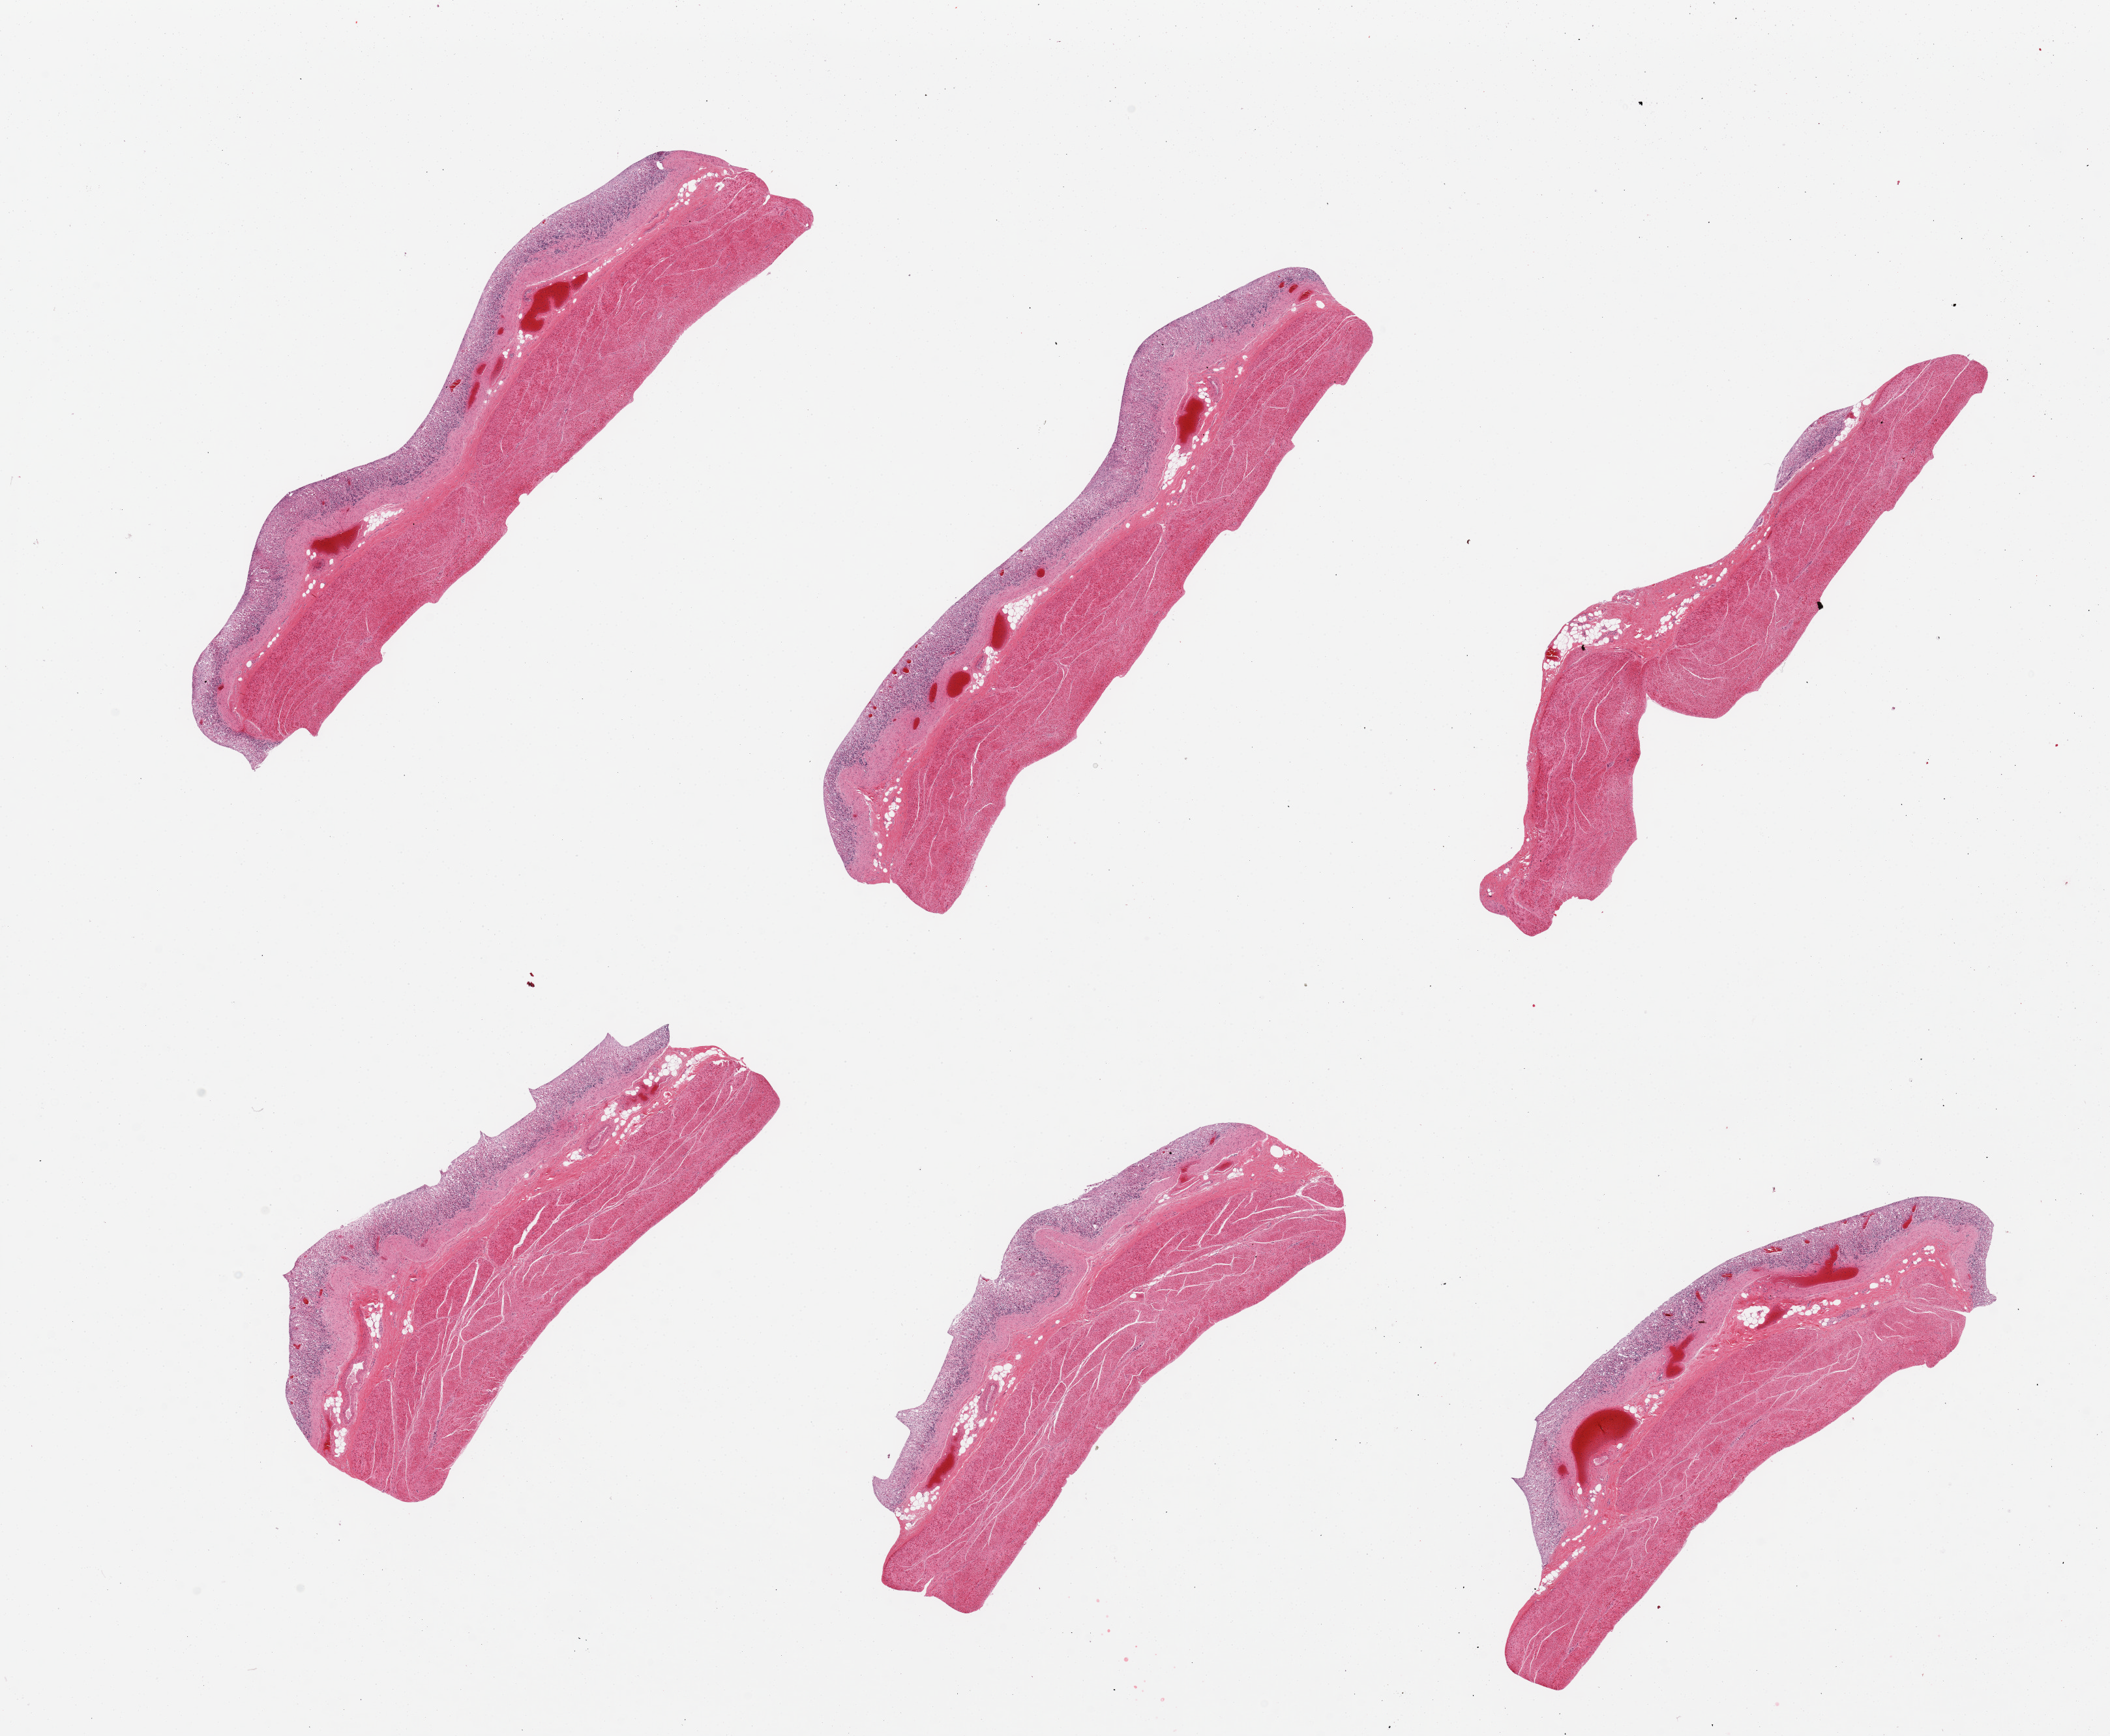
H&E whole-slide image, shown as a low-resolution overview of the whole scanned area (about 25.6 x 21.1 mm, slide scanned at 20x), PAXgene-fixed, paraffin-embedded tissue, target tissue: stomach, tissue donor sample. Female donor.
Review note (as recorded): 6 pieces, mucosa severely autolyzed (3), muscle less so (2).